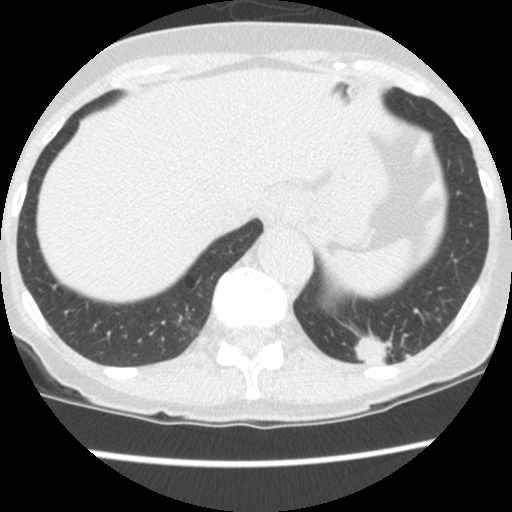
Low-dose screening chest CT, one axial slice; slice 26 of 130 in the series (ordered by position); reconstruction kernel STANDARD; 120 kVp; lung window (W 1500 / L -600 HU); 2.5 mm slice thickness; 512 × 512 image matrix, field of view 290 × 290 mm.
Annotated regions visible in this slice (manually delineated by an expert):
- lesion 1 (tumor, lower lobe of left lung): bounding box <353,334,395,364> (left, top, right, bottom; pixels)